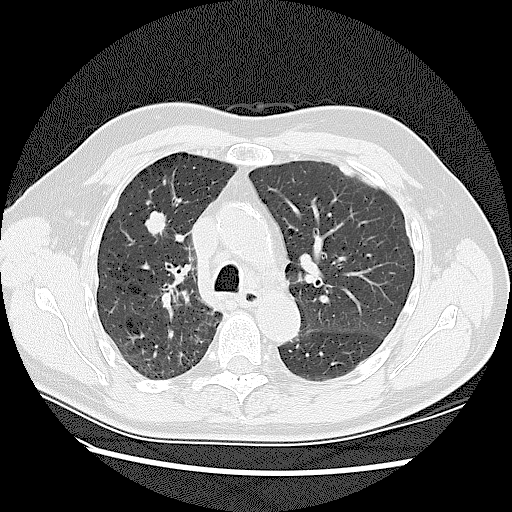
Low-dose screening chest CT, one axial slice; position 86 of 128 along the scan axis; reconstruction kernel LUNG; 120 kVp; lung window (W 1500 / L -600 HU); 2.5 mm slice thickness; 512 × 512 image matrix, field of view 360 × 360 mm.
Outlined on this slice (expert manual segmentation):
- lesion 1 (tumor, upper lobe of right lung): bounding box (x1, y1, x2, y2) in pixels: (145, 211, 166, 235)